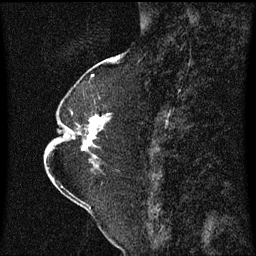
Breast MRI (dynamic contrast-enhanced), one sagittal slice; position 25 of 60 along the scan axis; dynamic contrast-enhanced series, image 2 of 3 at this slice position (ordered by acquisition); 1.5 T; TE 4.2 ms, TR 8.4 ms; 256 × 256 image matrix, field of view 200 × 200 mm. Patient: female, 52 years. Case-level facts recorded for this patient, not image findings: setting: breast cancer imaged before/during neoadjuvant chemotherapy; receptor status: HR-positive, HER2-negative.
Structures marked on this image (semi-automatically segmented with operator editing):
- analysis volume of interest (the breast-tissue region the enhancement analysis was run in; not a lesion): bounding box <64,112,112,167> (left, top, right, bottom; pixels)
- tumour enhancement mask (voxels above the 70 % enhancement threshold inside the analysis volume of interest): <83,114,111,159>